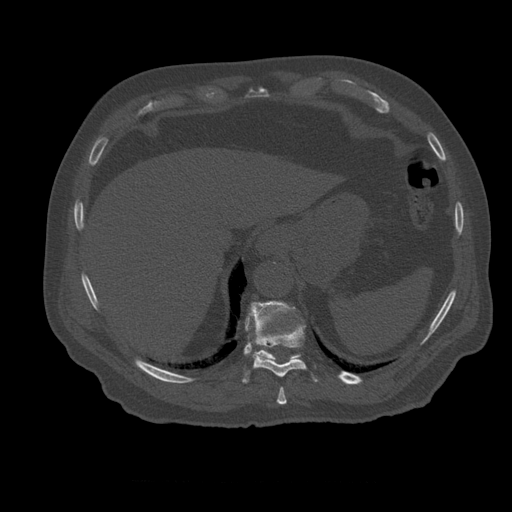
CT including the spine, one axial slice. Slice 298 of 399 in the series (ordered by position). Bone window (W 1800 / L 400 HU). 1.25 mm slice thickness. 512 × 512 image matrix. Patient age 73 years. From the clinical record (not read from this slice): primary cancer: prostate; vertebrae with lytic lesions (as recorded): L2.
Annotated regions visible in this slice (semi-automatic segmentation, software-assisted and operator-edited):
- T10 vertebra: box from (x=243, y=324) to (x=318, y=383) px
- T11 vertebra: (x=245, y=301)–(x=301, y=361)
- T9 vertebra: (x=277, y=388)–(x=287, y=405)